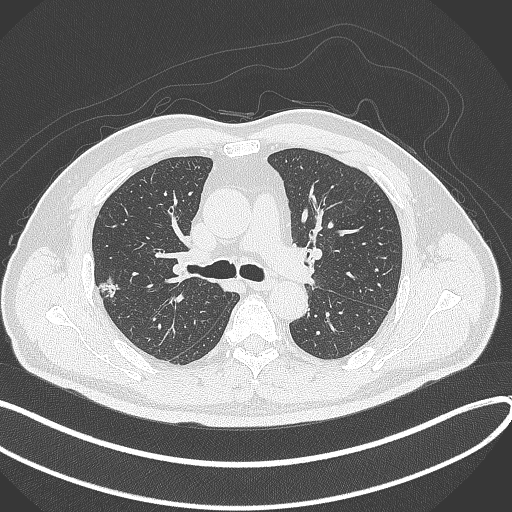
Chest CT, one axial slice. Position 217 of 372 along the scan axis. Reconstruction kernel B70f. 120 kVp. Lung window (W 1500 / L -600 HU). 512 × 512 image matrix, field of view 400 × 400 mm. Patient: male, 60 years. Case-level facts recorded for this patient, not image findings: clinical TNM (as recorded): T1c N0 M0.
Structures marked on this image (rectangle marked by the reading radiologist):
- lung tumour (recorded histology: adenocarcinoma): bounding box <94,273,123,305> (left, top, right, bottom; pixels)